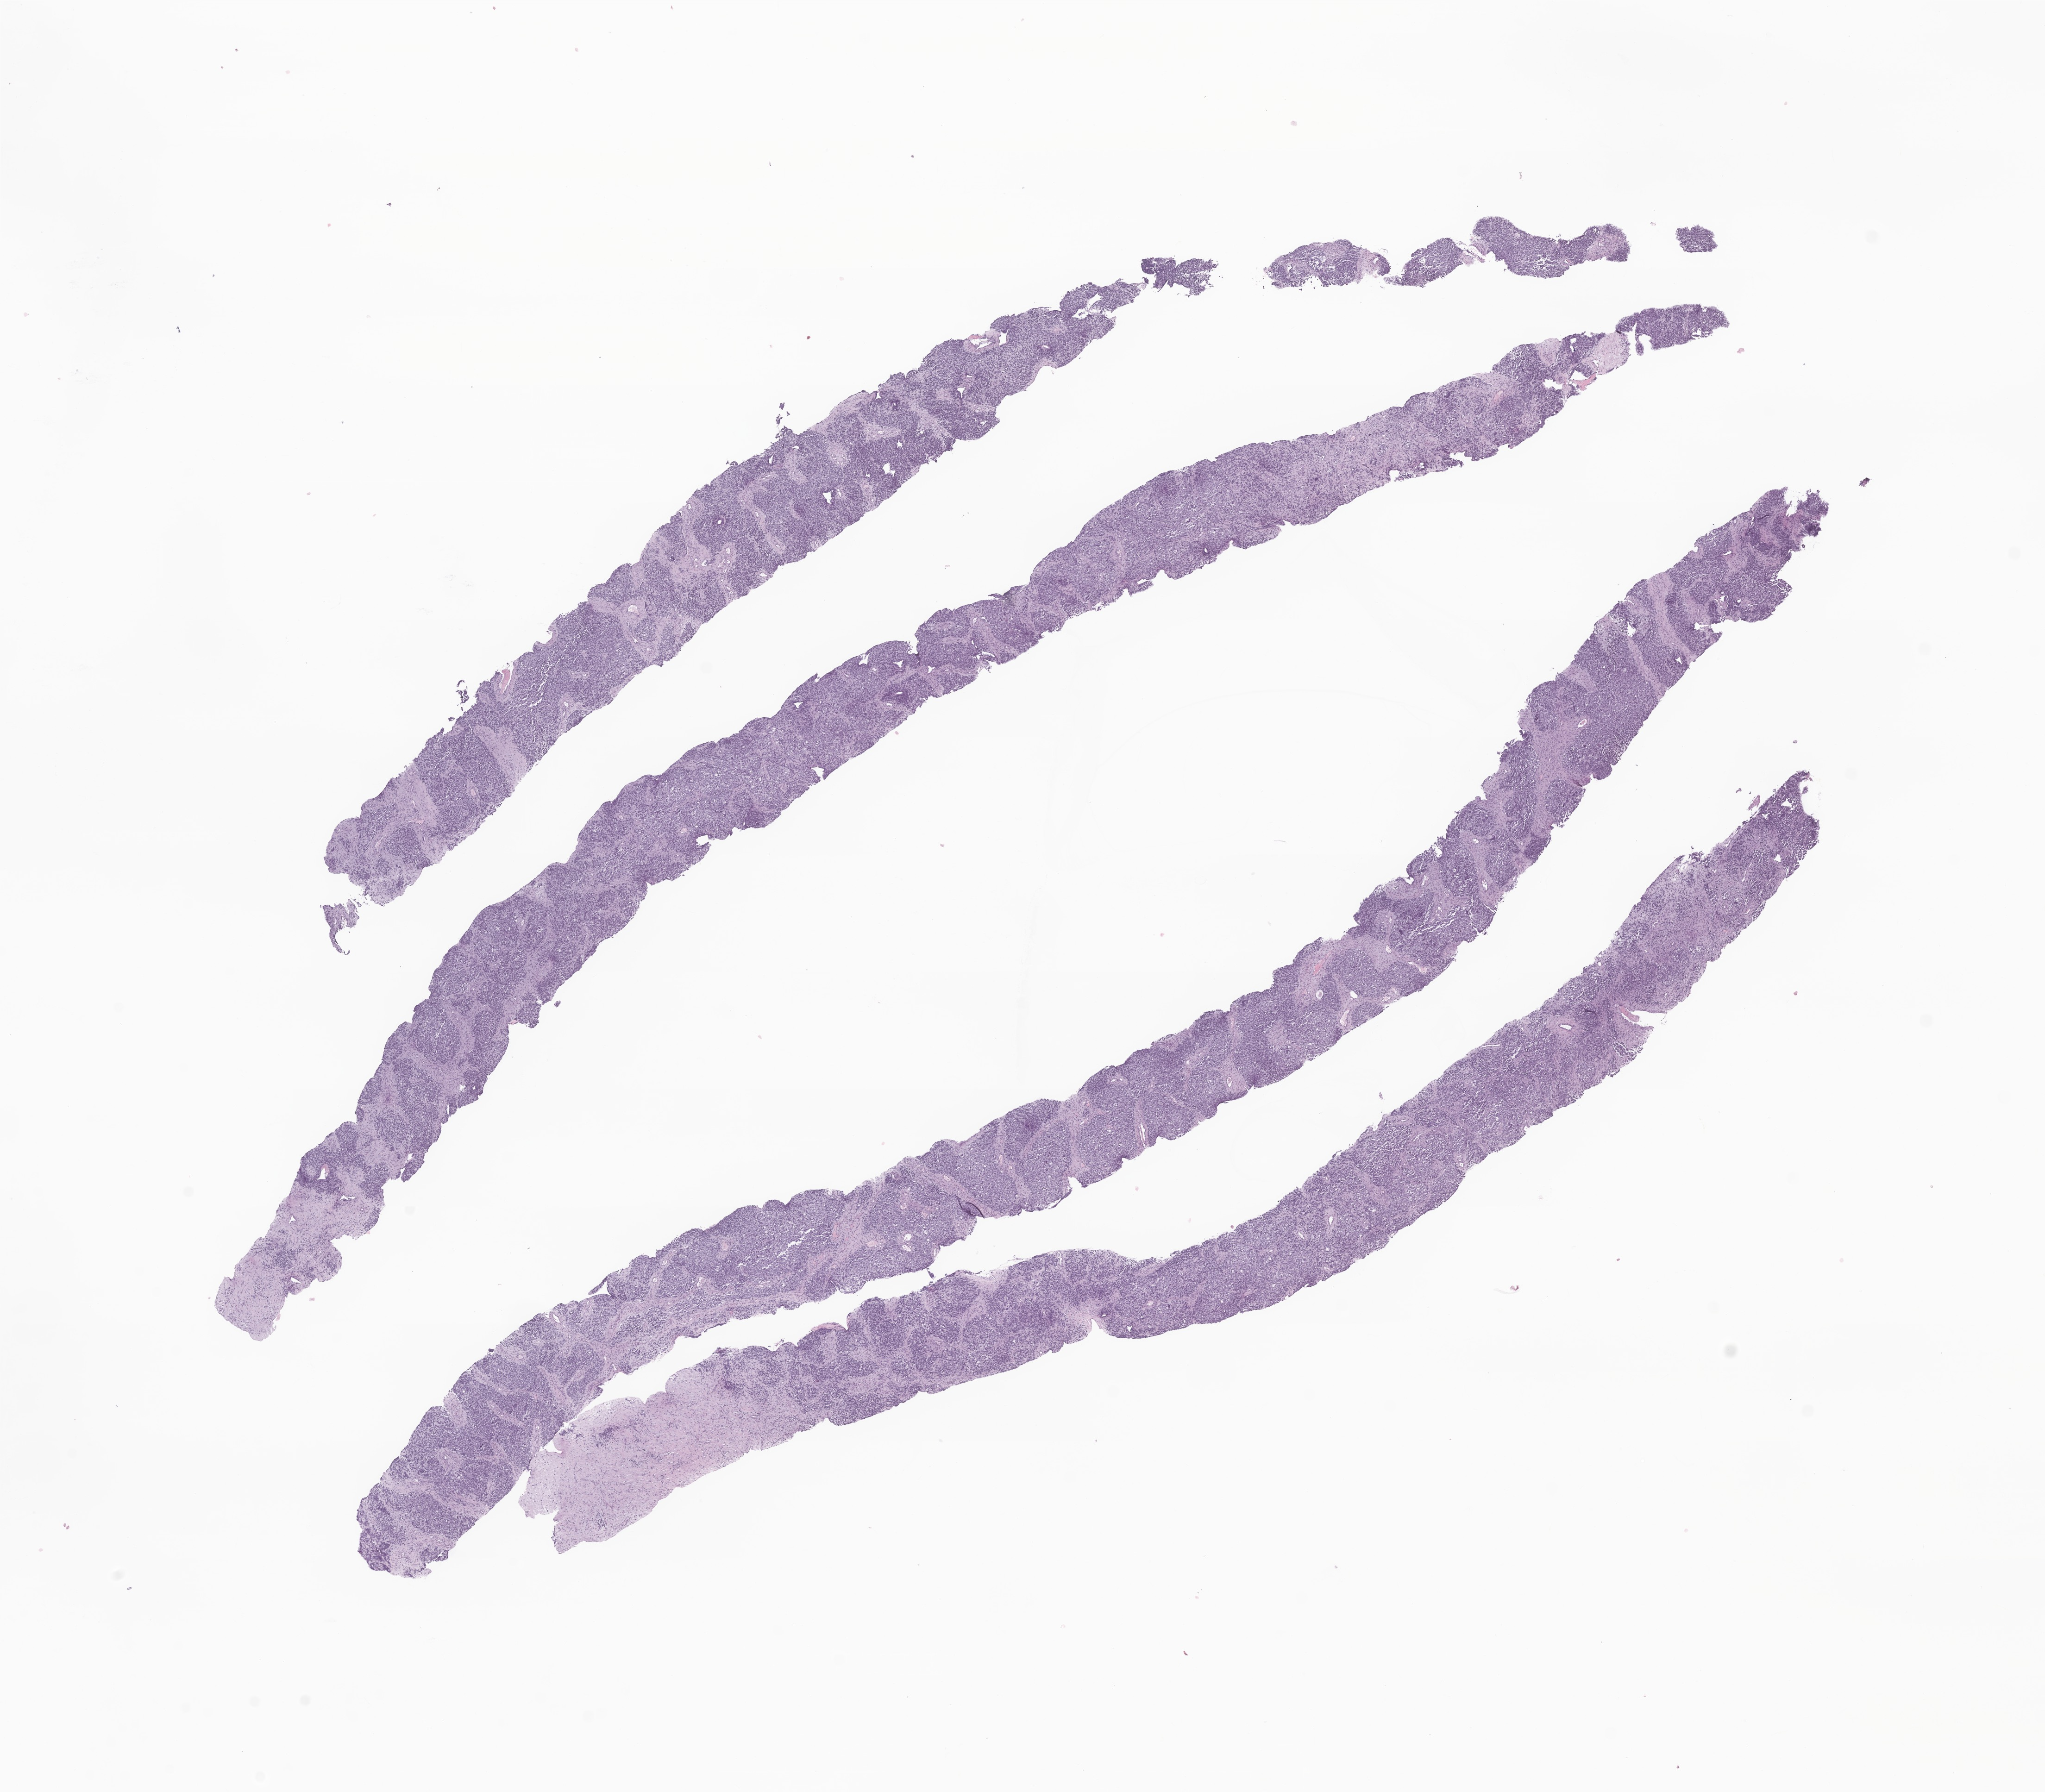
Haematoxylin and eosin whole-slide image of tumor tissue from the abdomen — low-resolution overview of the scanned area, about 18.6 x 16.3 mm; formalin-fixed, paraffin-embedded (FFPE) tissue. Female patient, age 34 months (2 years 10 months).
Diagnosis (ICD-O-3 morphology term): Rhabdomyosarcoma, NOS.